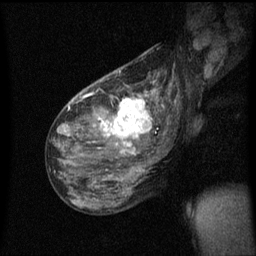
Breast MRI (dynamic contrast-enhanced), one sagittal slice; position 33 of 60 along the scan axis; dynamic contrast-enhanced series, image 2 of 3 at this slice position (ordered by acquisition); 1.5 T; TE 4.2 ms, TR 8.4 ms; 256 × 256 image matrix, field of view 200 × 200 mm. Patient: female, 49 years.
Outlined on this slice (semi-automatically segmented with operator editing):
- analysis volume of interest (the breast-tissue region the enhancement analysis was run in; not a lesion): box from (x=103, y=90) to (x=157, y=151) px
- tumour enhancement mask (voxels above the 70 % enhancement threshold inside the analysis volume of interest): (x=103, y=92)–(x=154, y=151)